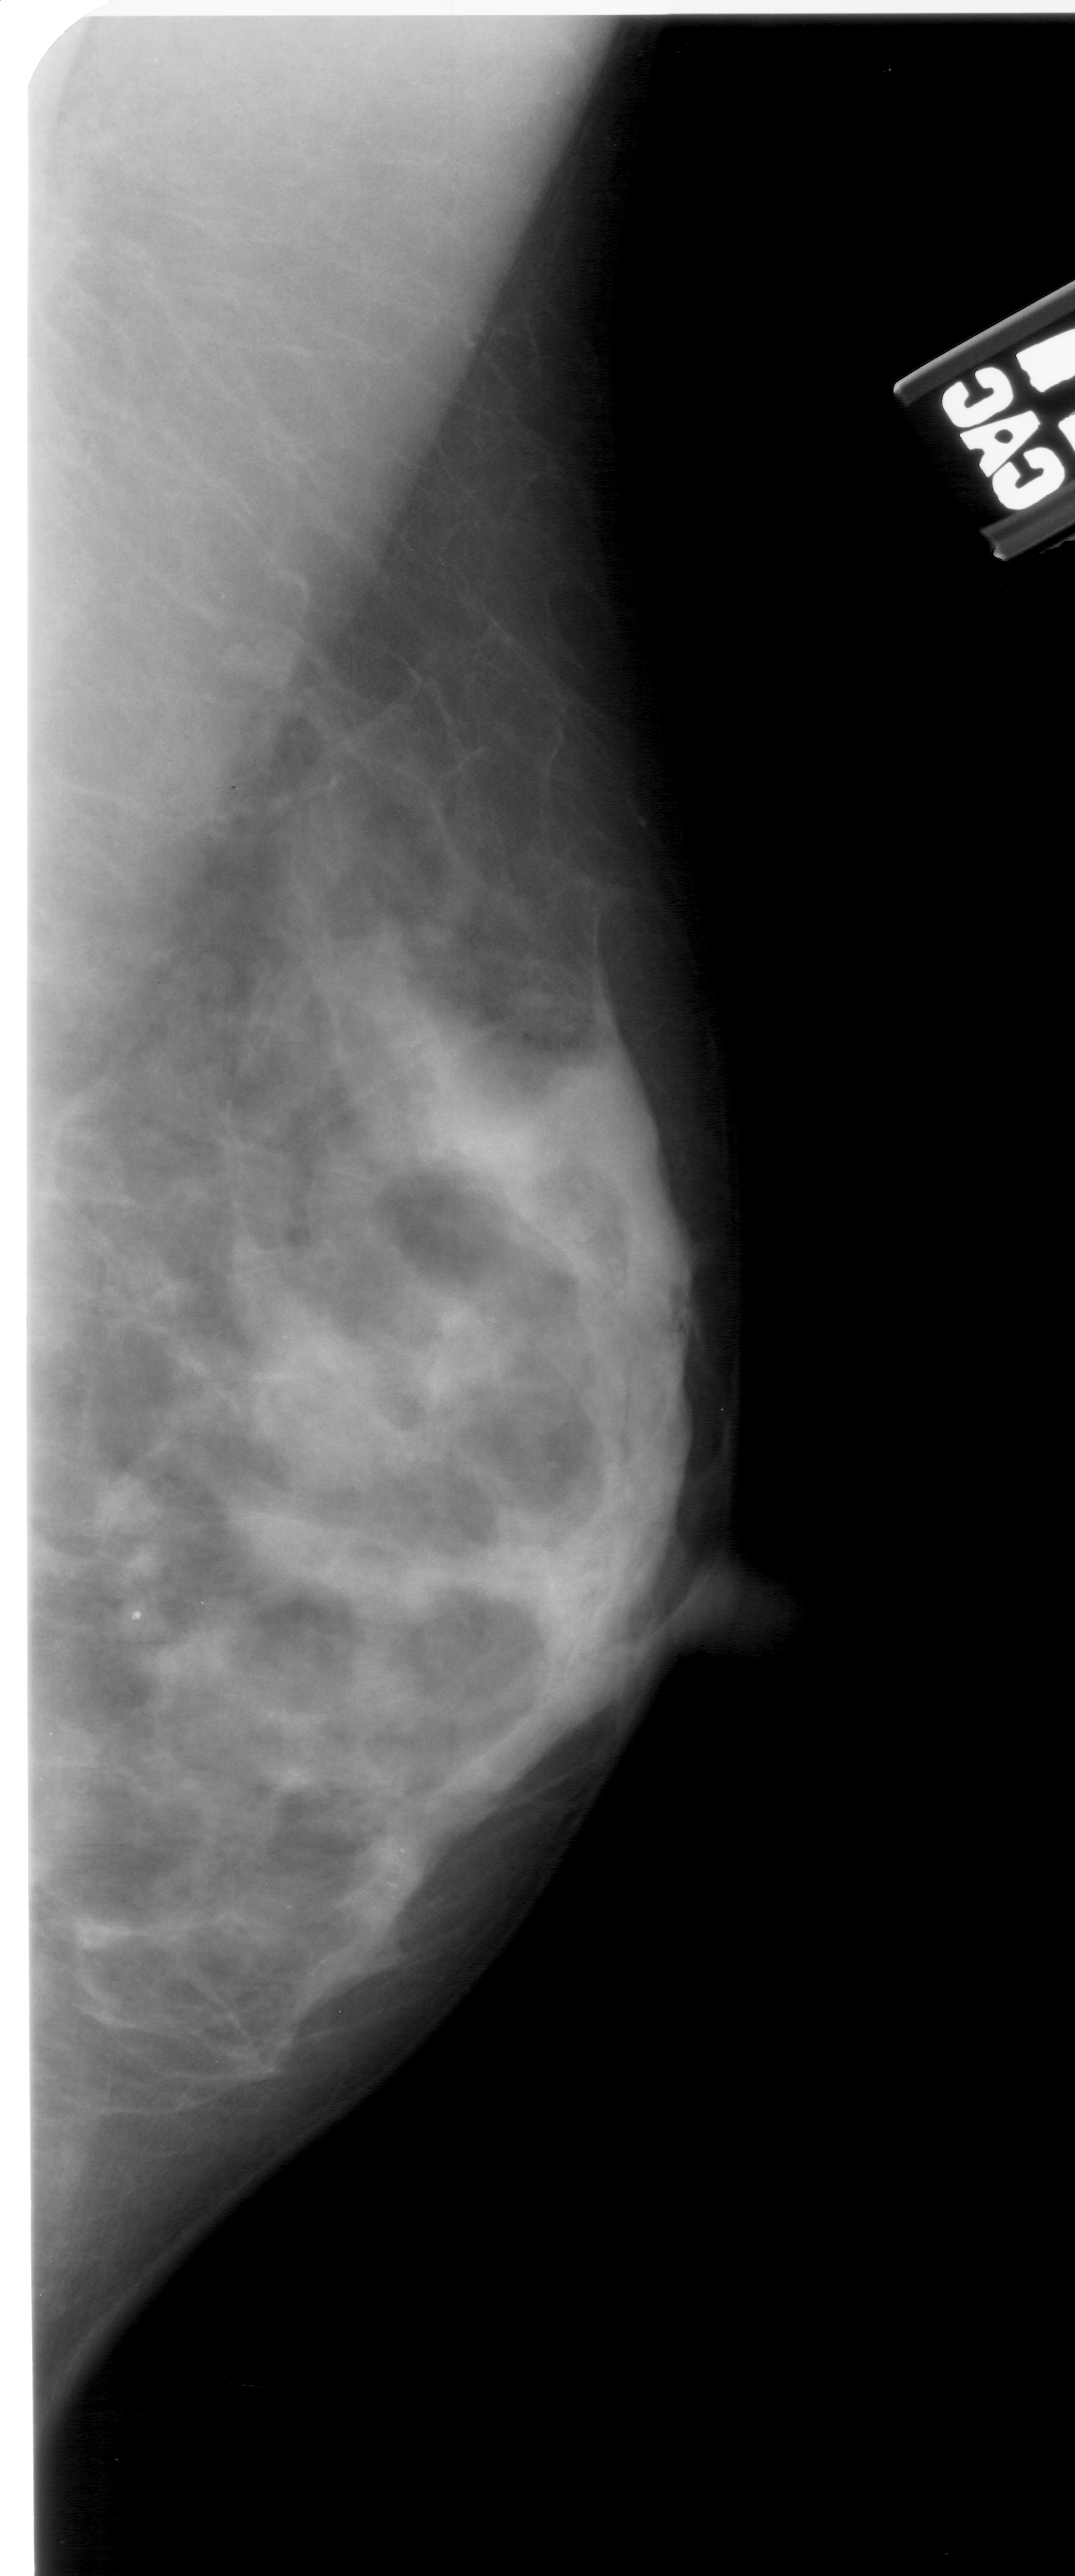
Digitized screen-film mammogram; right breast; mediolateral oblique (MLO) view; breast composition: extremely dense (BI-RADS density category 4 of 4).
- Finding: calcifications, morphology pleomorphic, distribution clustered; BI-RADS assessment category 4; pathology result (as recorded, not read from the image): benign.